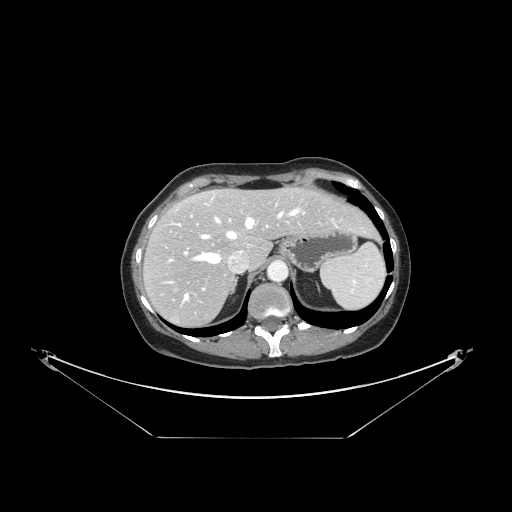
Contrast-enhanced abdominal CT, one axial slice; position 114 of 148 along the scan axis; reconstruction kernel STANDARD; soft-tissue window (W 400 / L 40 HU); 512 × 512 image matrix, field of view 500 × 500 mm. Female patient, age 73 years. Case-level facts recorded for this patient, not image findings: diagnosis: colorectal cancer liver metastases, imaged before liver resection; multiple liver metastases: no; largest metastasis: 1 cm; chemotherapy before resection: yes.
Structures marked on this image (manually delineated by an expert):
- hepatic veins: bounding box <178,208,305,302> (left, top, right, bottom; pixels)
- liver: <145,189,374,326>
- planned liver remnant (the part of the liver to remain after resection): <169,190,375,264>
- portal vein (with intrahepatic branches): <184,215,231,291>